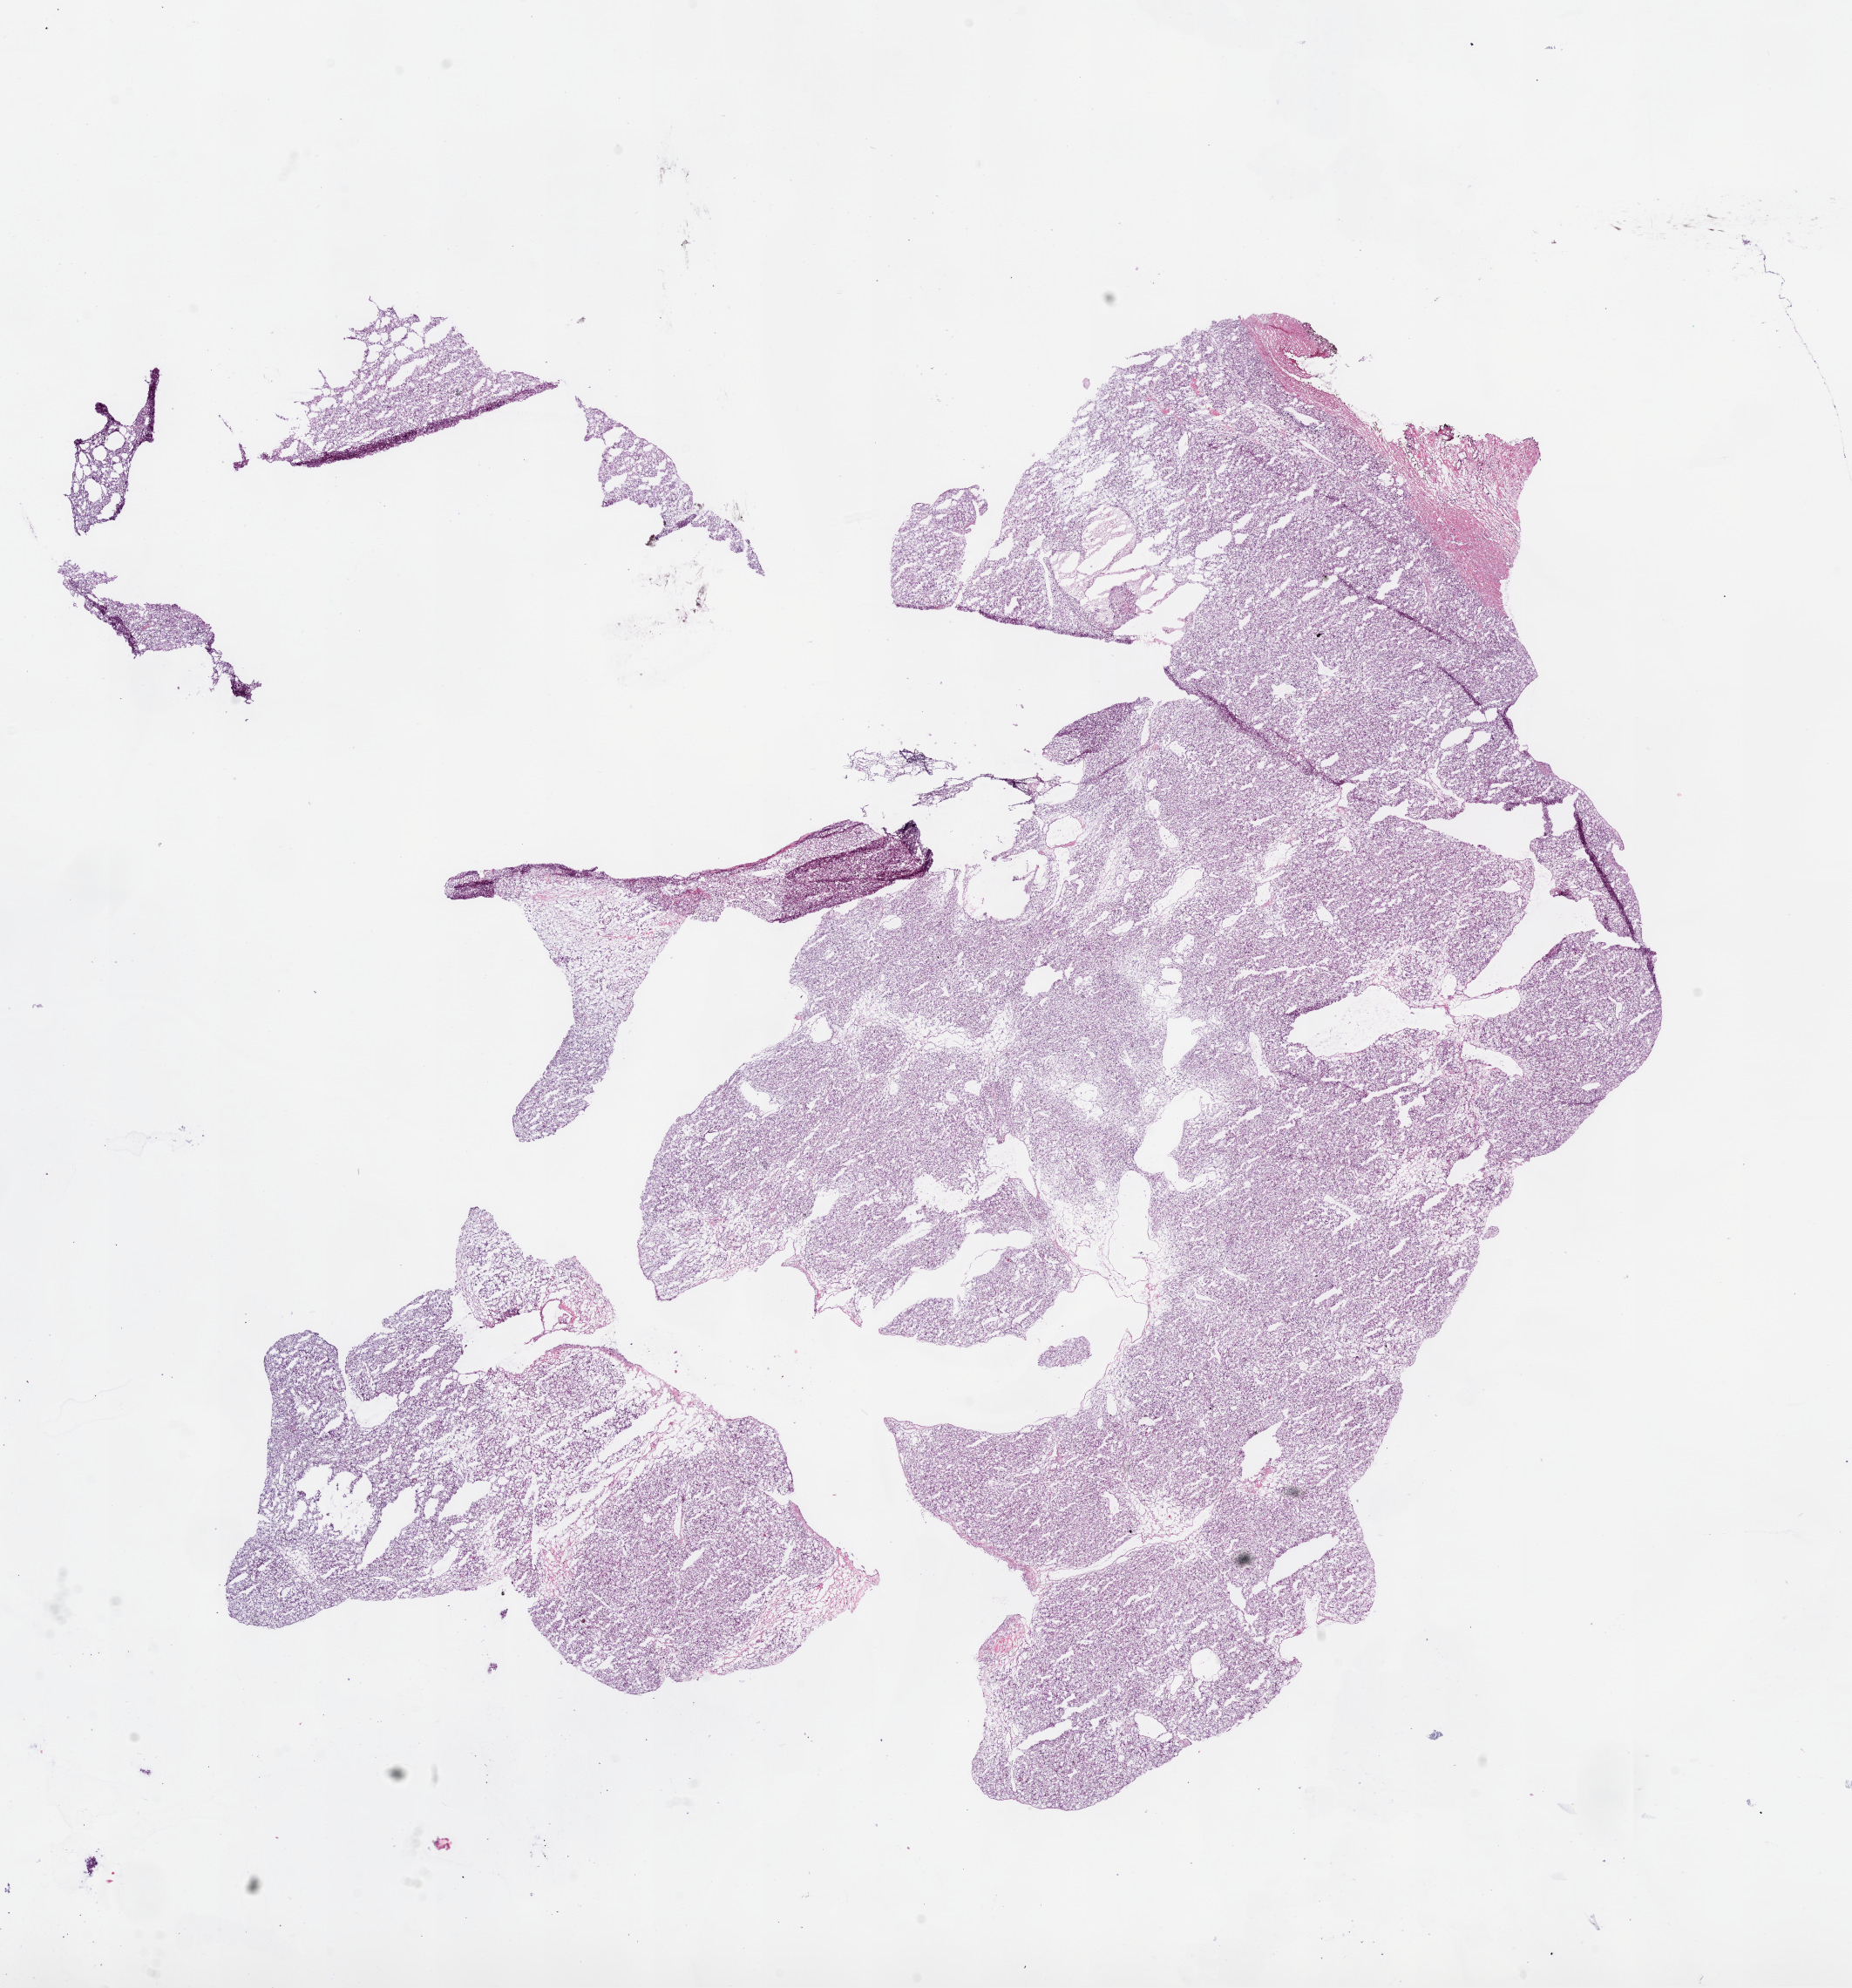
H&E-stained whole-slide image — whole scanned area (about 17.1 x 18.3 mm) shown as a low-resolution overview; frozen section from the bottom of the tissue portion; primary tumour sample from the kidney. Male patient; age at initial diagnosis 74 years. Pathologist review of this section (percent, as recorded): tumour cells 95%, tumour nuclei 85%.
Diagnosis: Clear cell adenocarcinoma, NOS.